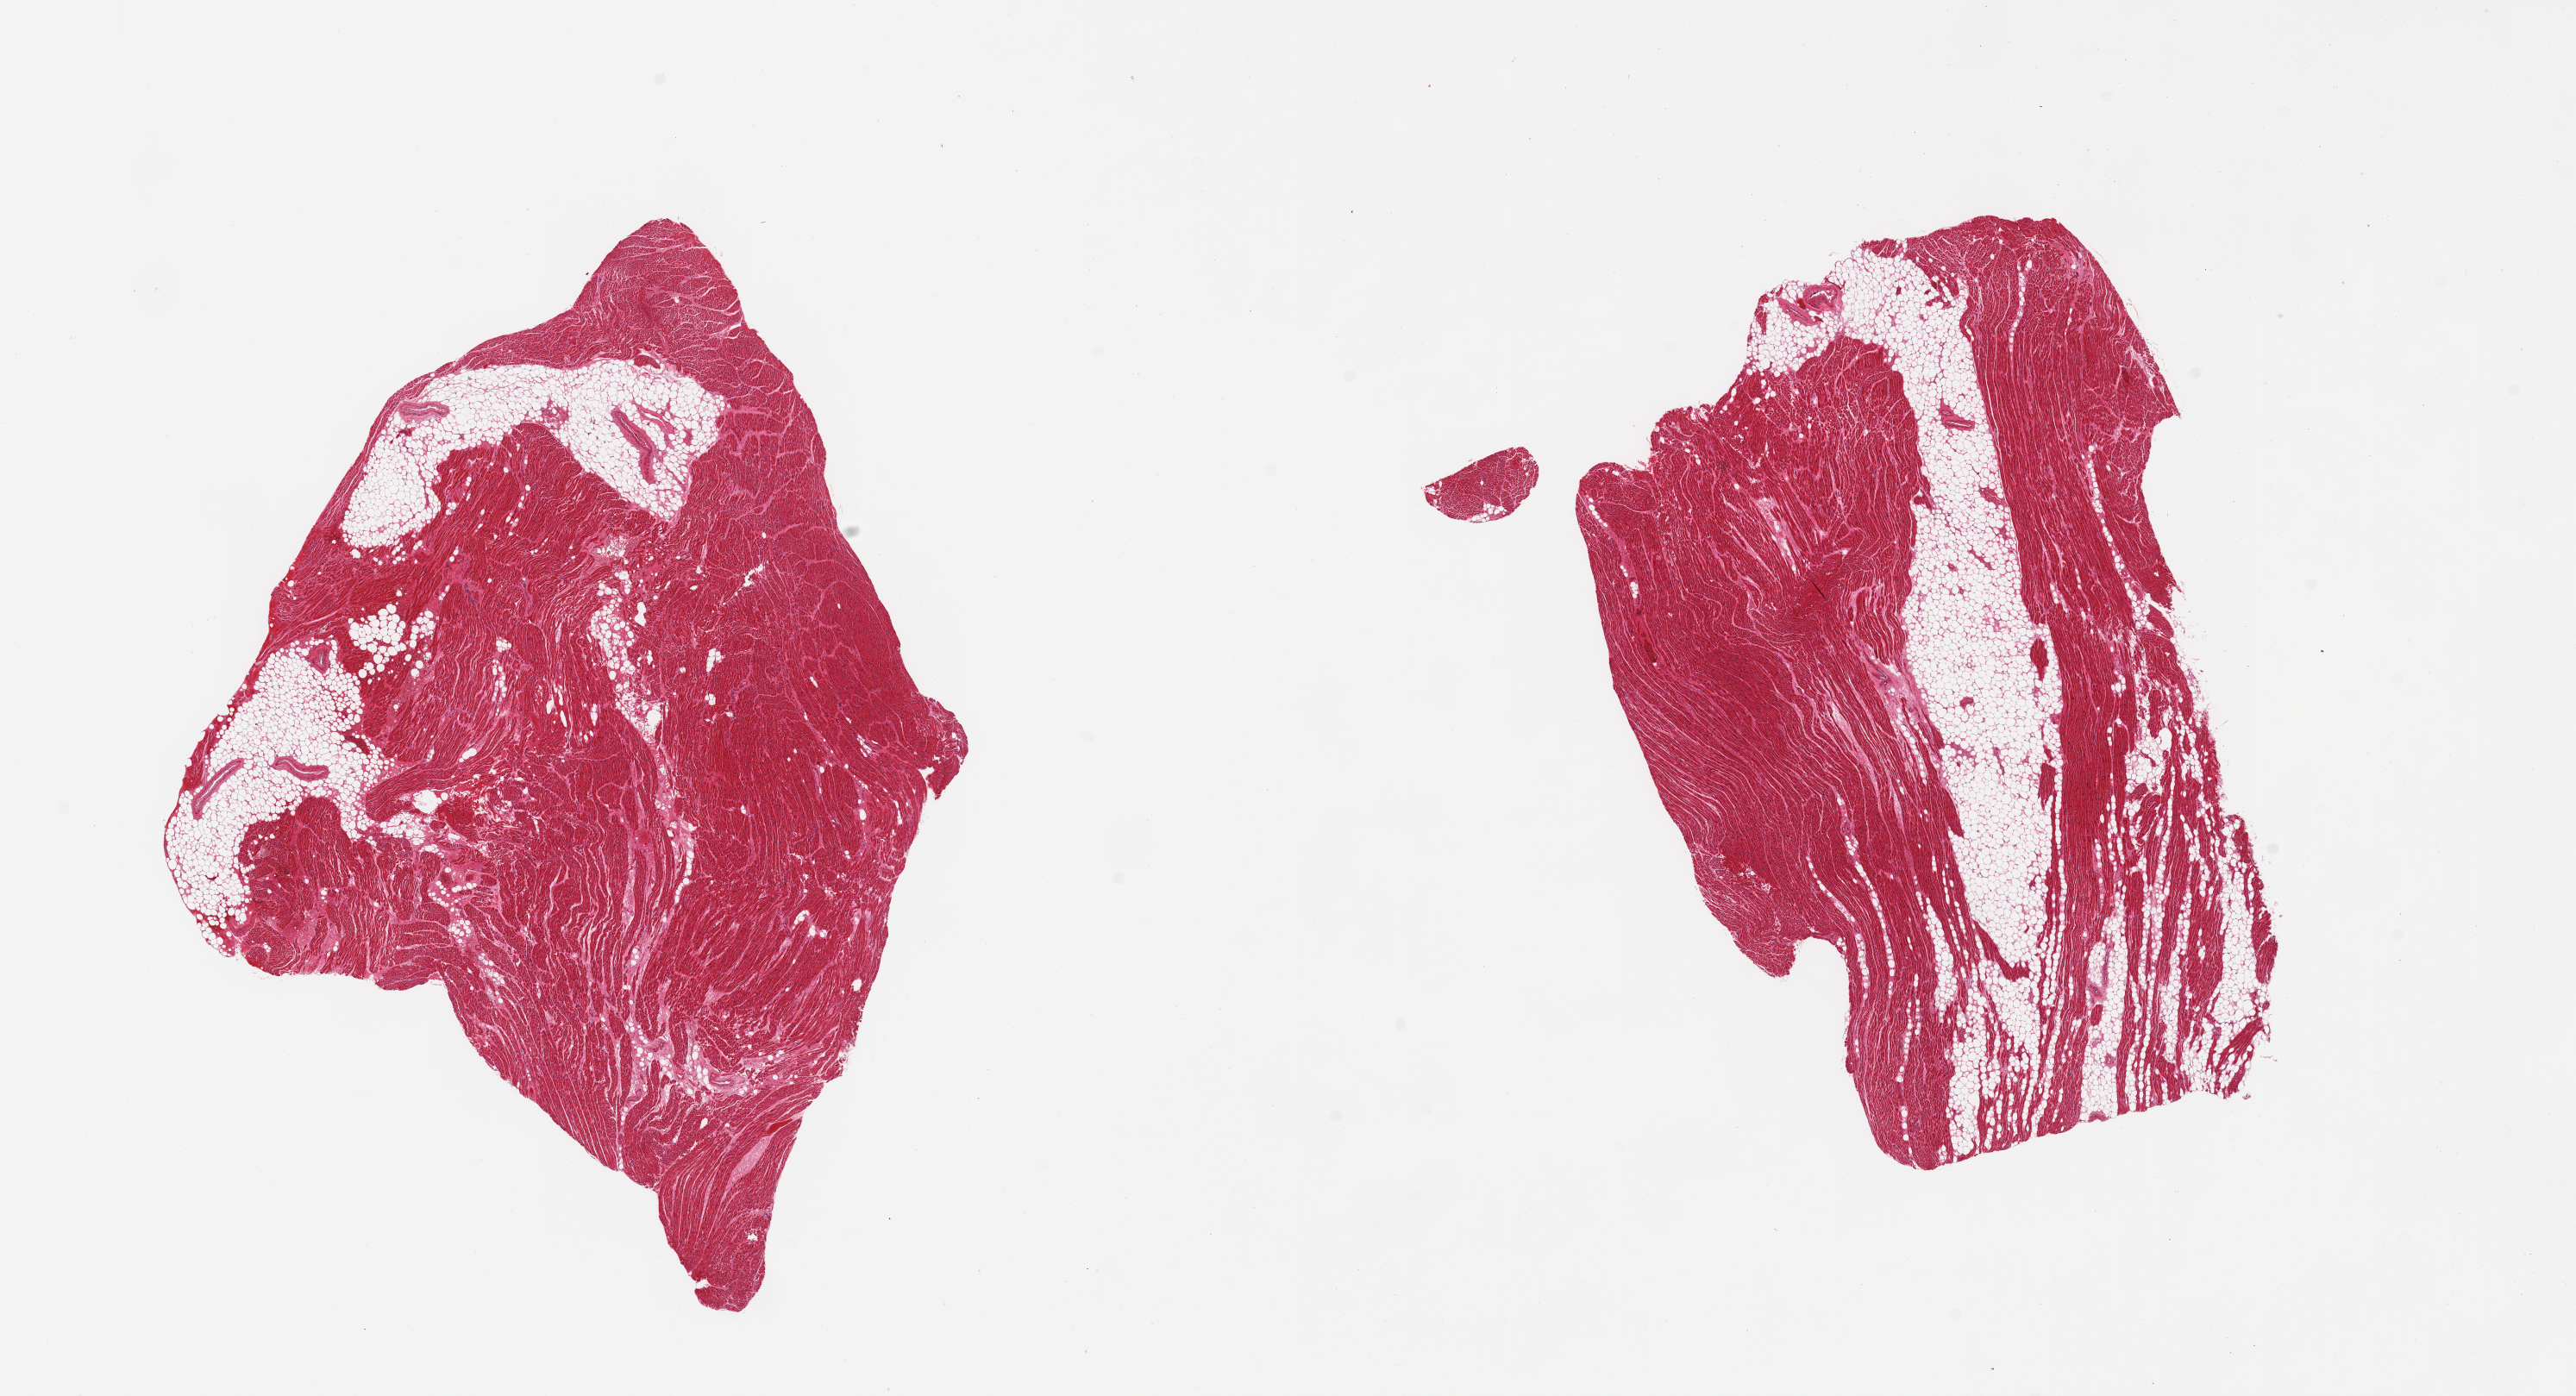
Digitized H&E-stained section — a low-resolution overview of the entire scanned area, about 23.6 x 12.8 mm. PAXgene-fixed, paraffin-embedded tissue. Target tissue: auricular appendage. Donor tissue sample. Donor sex: male.
• reviewer comment on this tissue sample: 2 pieces, no abnormalities